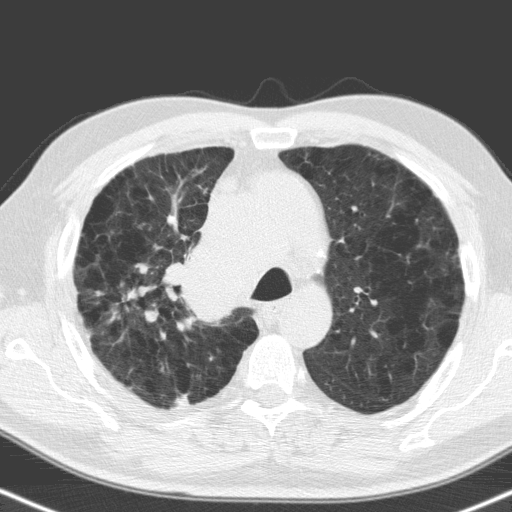
Low-dose screening chest CT, one axial slice. Slice 119 of 160 in the series (ordered by position). Lung window (W 1500 / L -600 HU). 3.2 mm slice thickness. 512 × 512 image matrix, field of view 324 × 324 mm.
Outlined on this slice (manually delineated by an expert):
- lesion 1 (tumor, hilum of right lung): bounding box (x1, y1, x2, y2) in pixels: (166, 237, 239, 320)